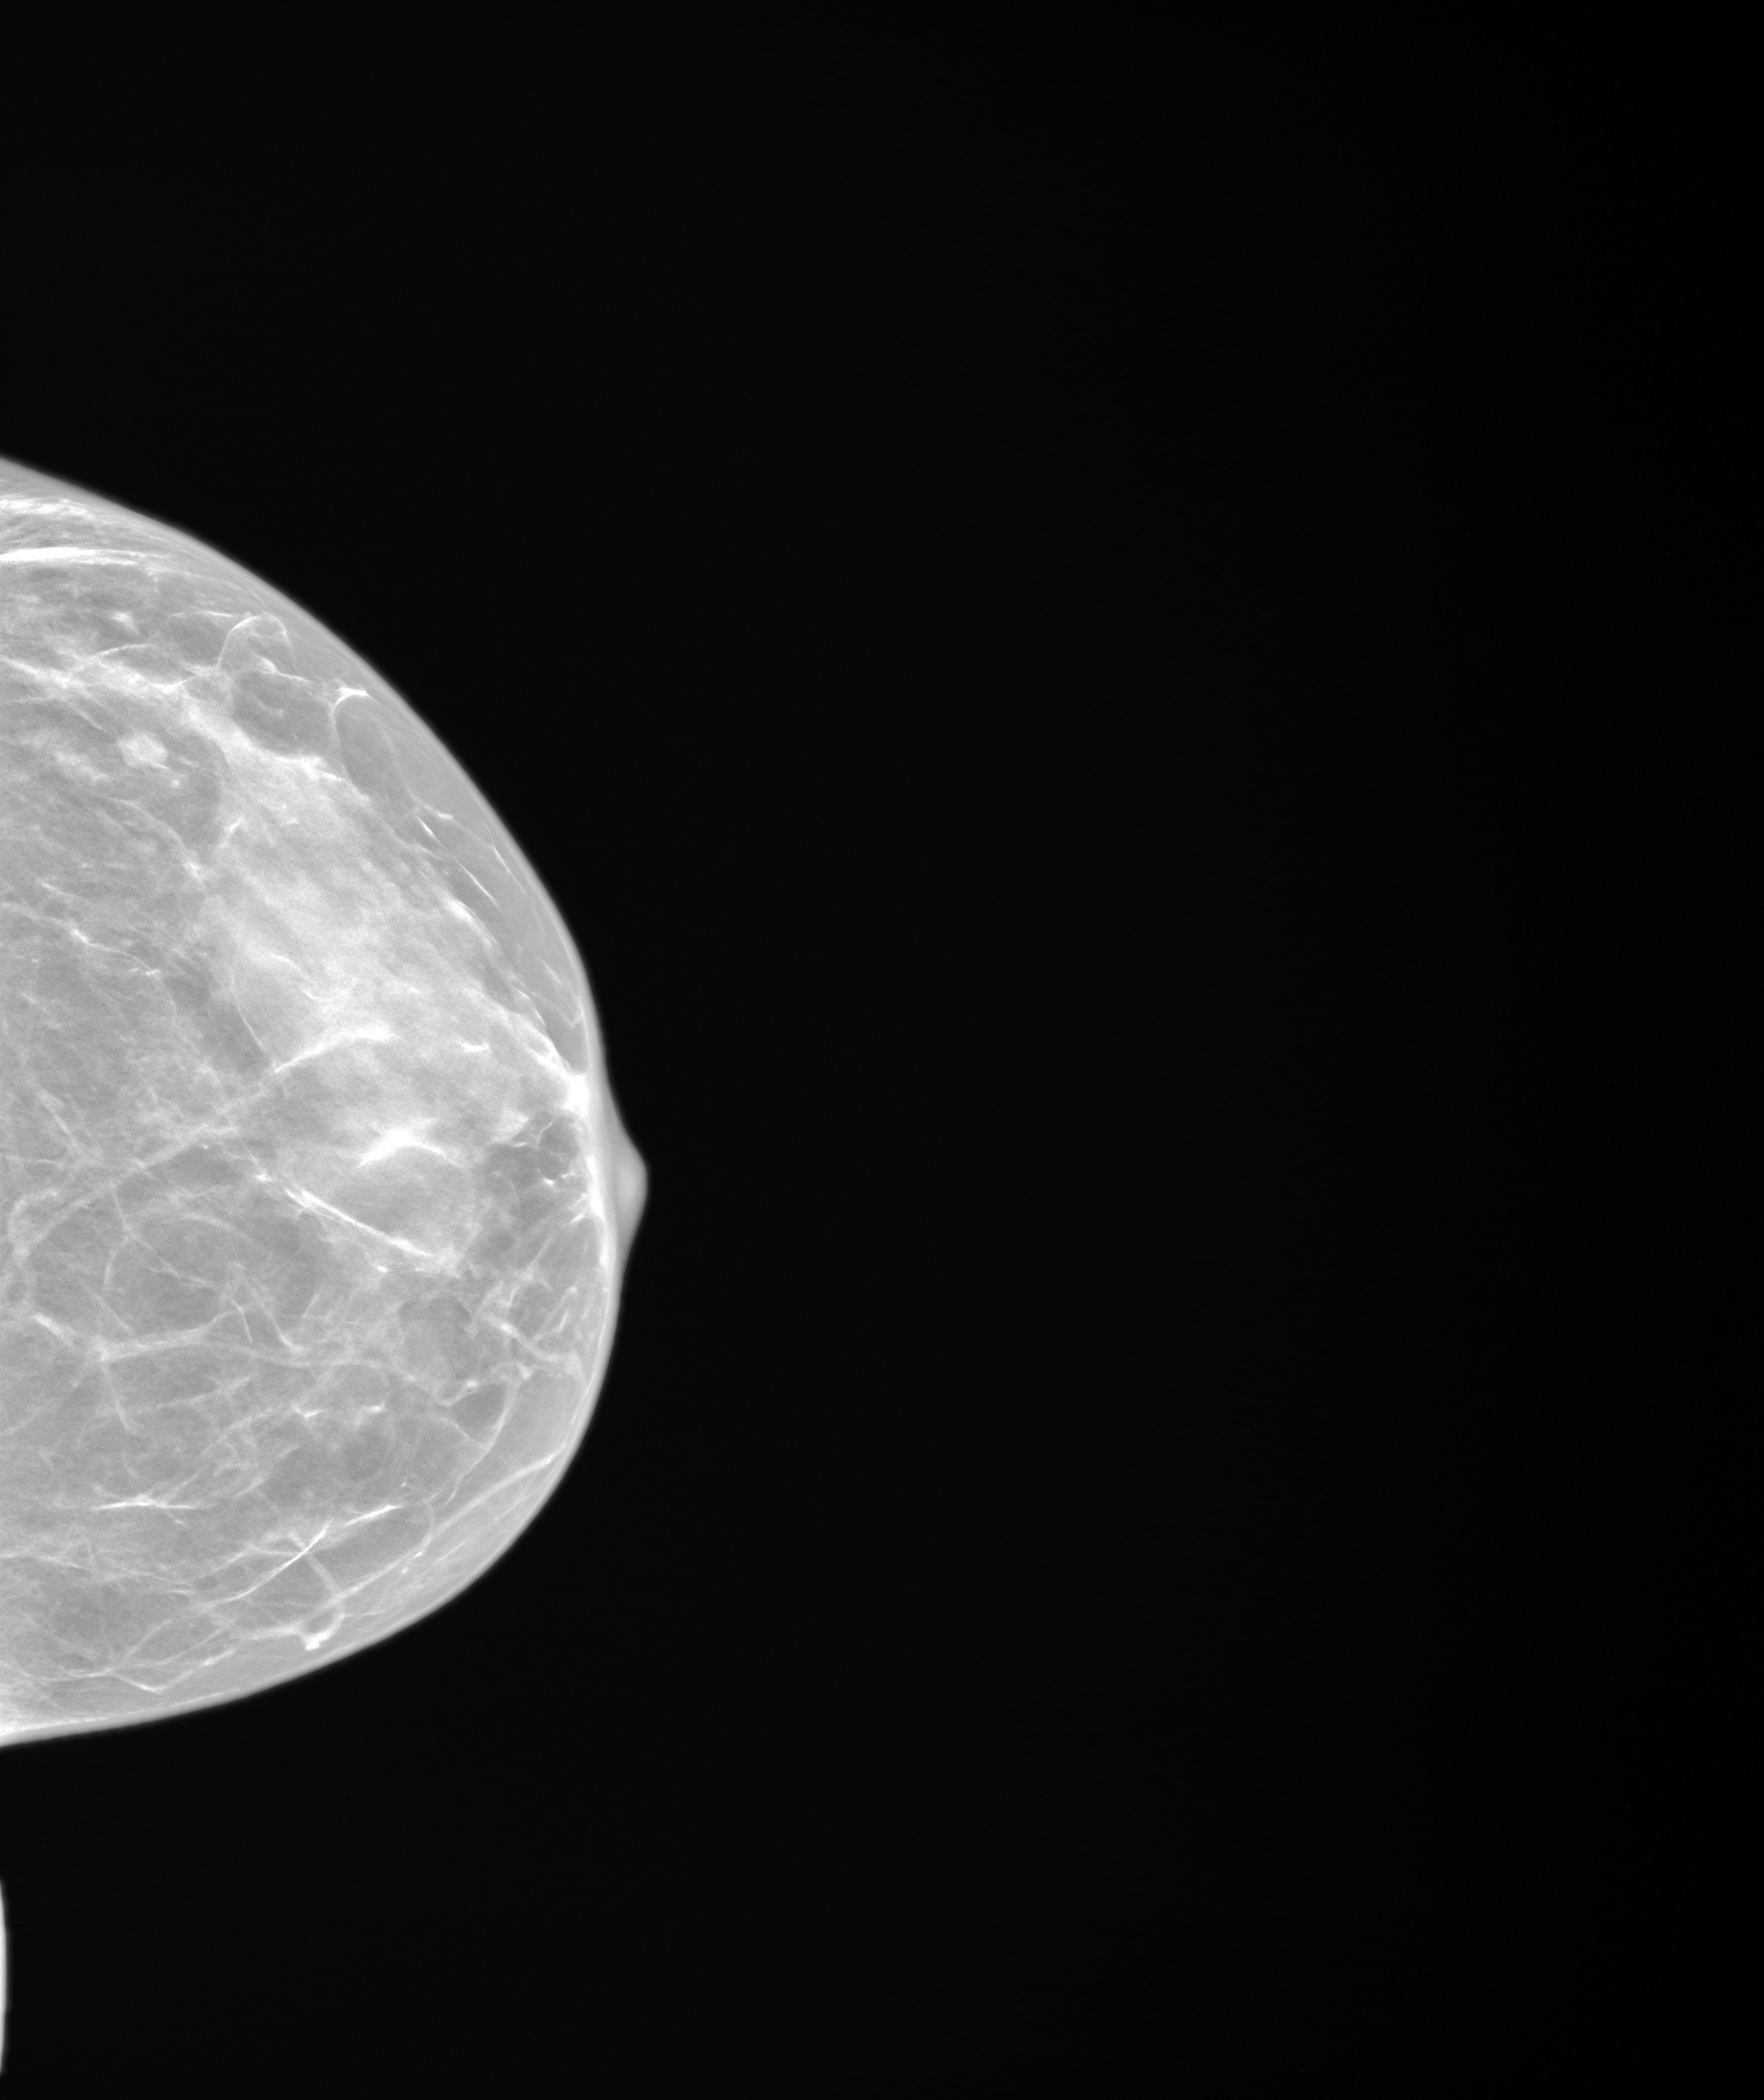
Annual screening mammography examination, system: SenoIris_1SP1.1(421). Patient: female, 47 years.
Image type: synthesized 2-D view from tomosynthesis. Breast: left. Projection: cranio-caudal projection. BI-RADS breast density category at the screening exam (both breasts, scale 1–4): 3. Final BI-RADS category for the screening round (tomosynthesis exam, both breasts): category 2. Recall: no recall after this screen.